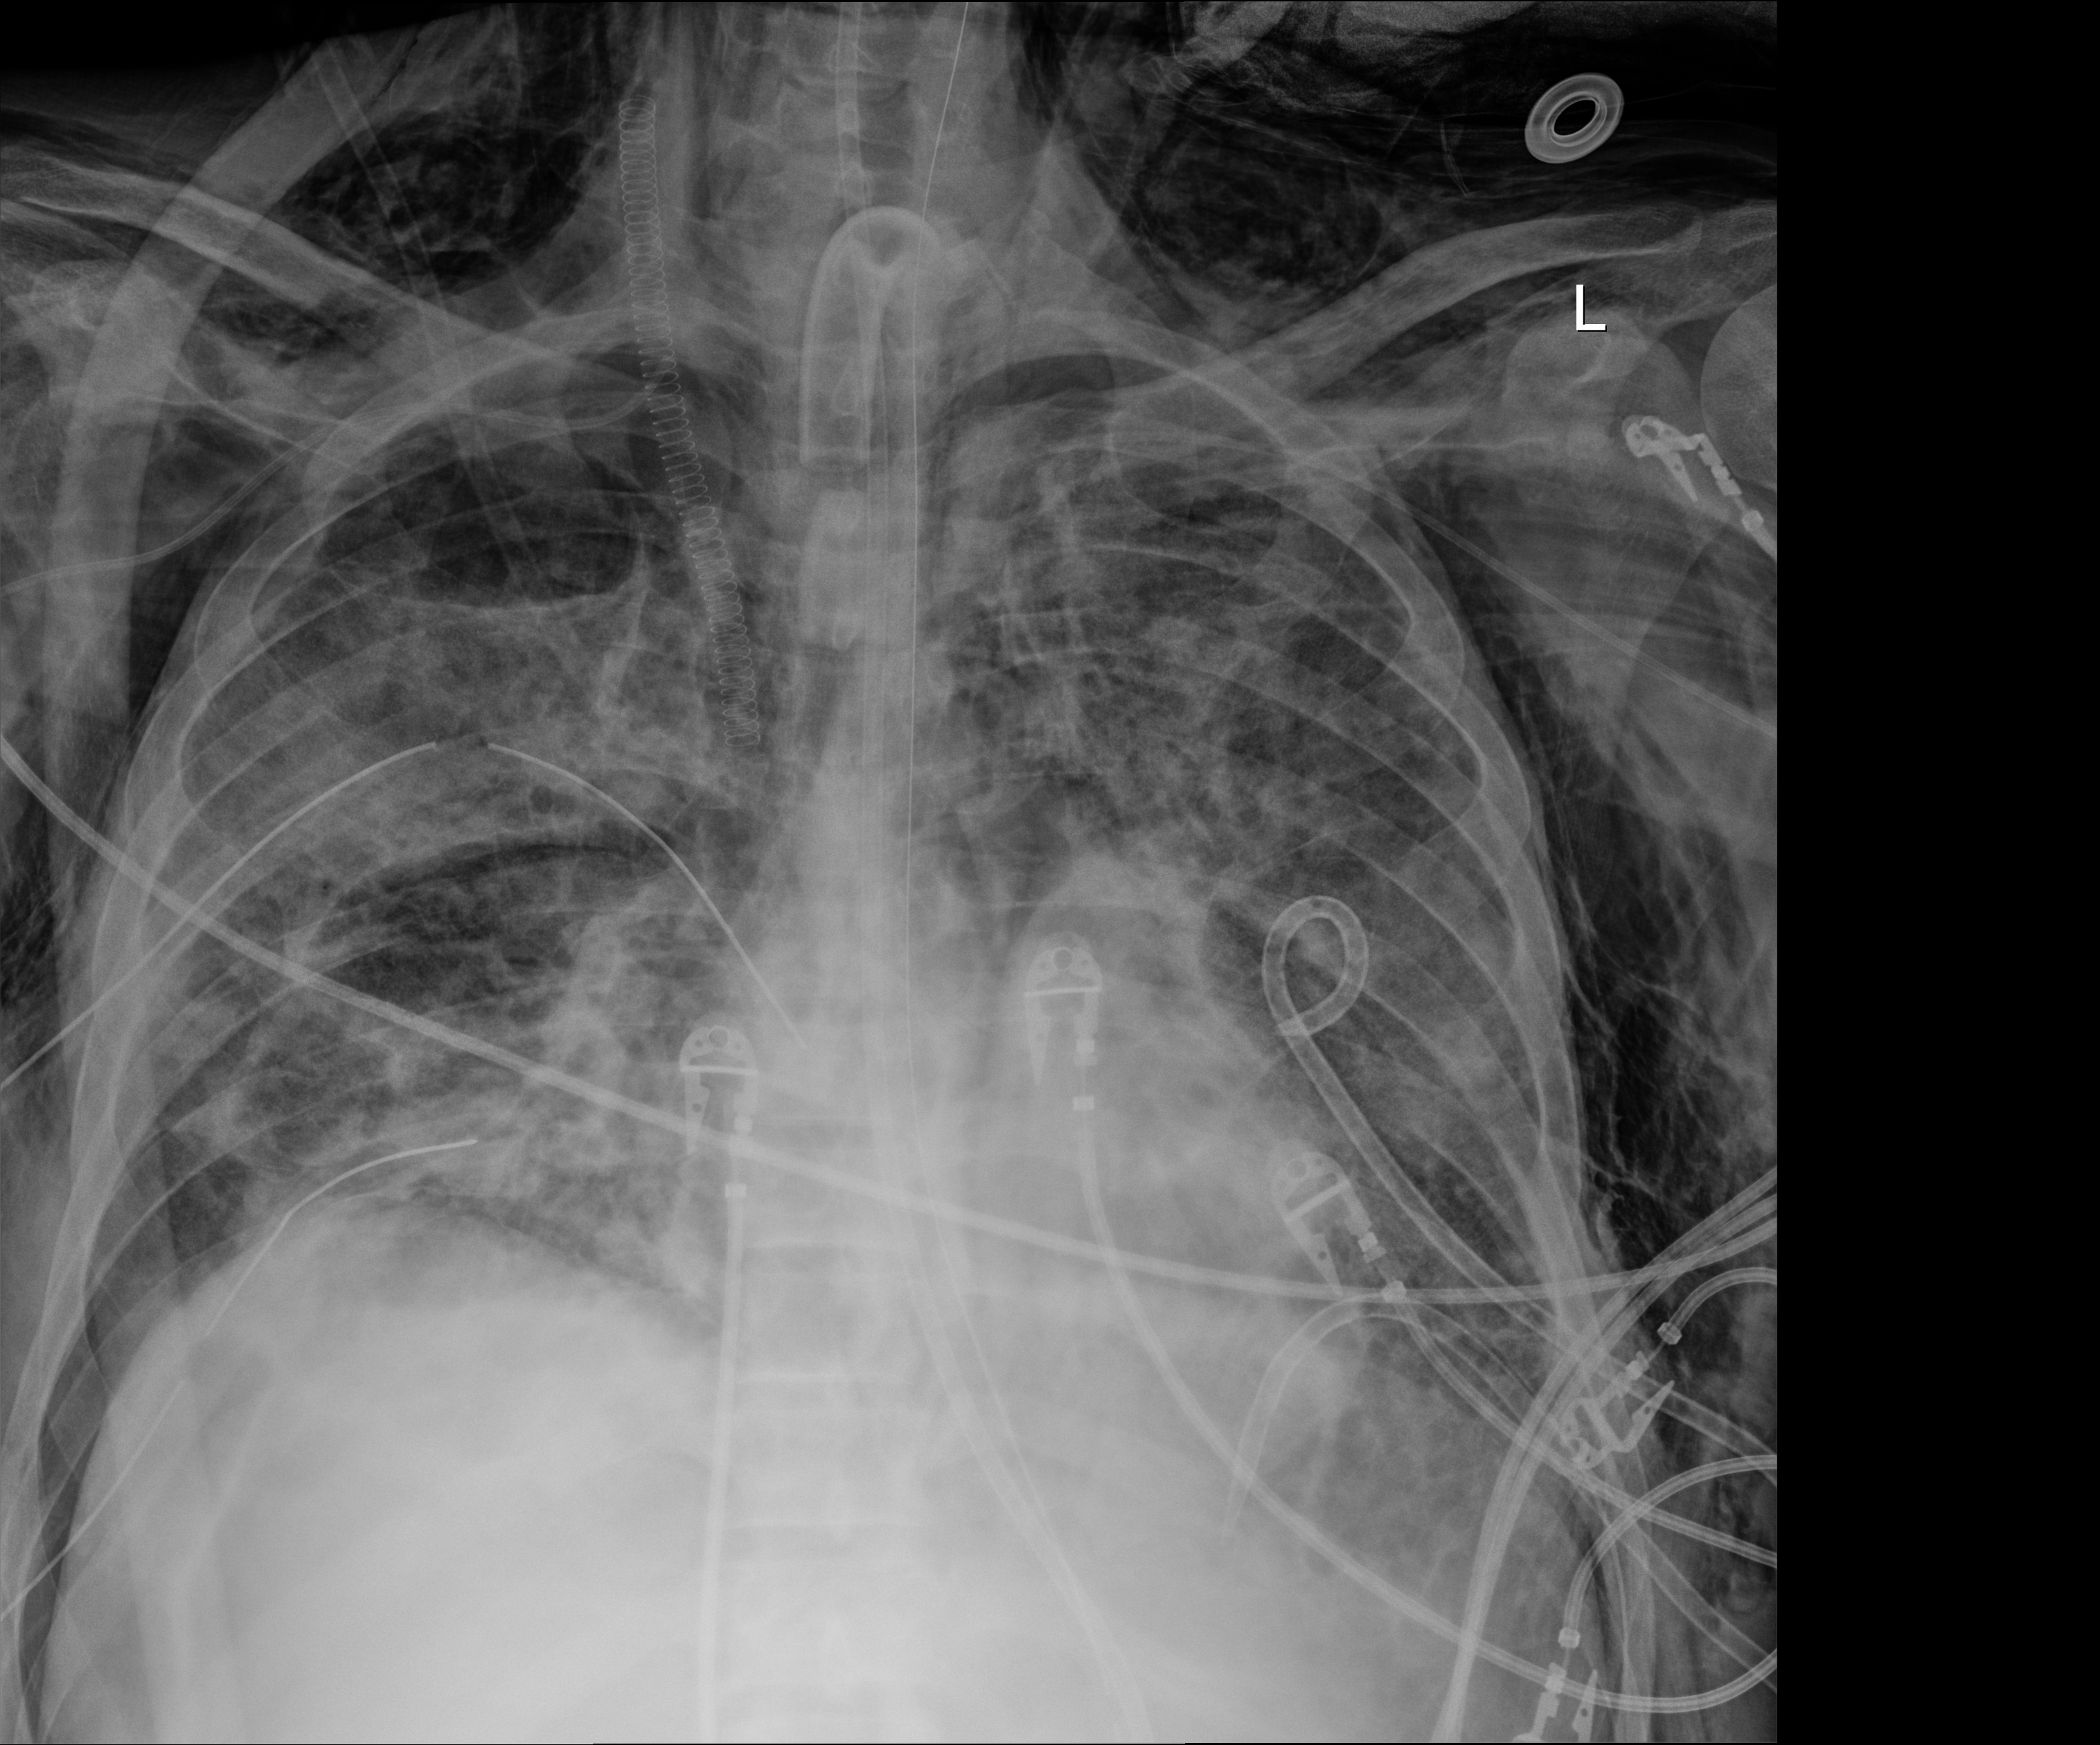
Chest radiograph (digital radiography); anteroposterior (AP) projection. Patient hospitalised with COVID-19, aged 18–59 years.
Admission-level facts for this patient (not findings on this image; timing relative to this image not recorded): length of hospital stay: 60 days; COPD (admission record): no.